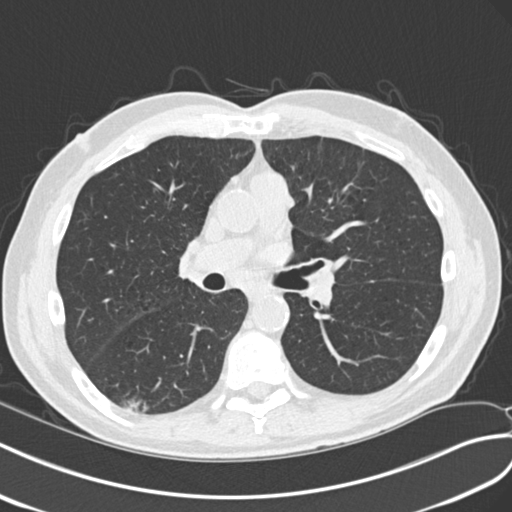
Low-dose screening chest CT, axial slice. Second screening round (one year after baseline). Lung window (W 1500 / L -600 HU). 2 mm slice thickness. Male, age 68 years at enrolment.
- Expert-annotated lung lesion, bounding box <112,385,162,422> (left, top, right, bottom; pixels).
- The screening reader recorded 4 non-calcified nodules or masses ≥4 mm on this exam; which of them this box marks is not recorded.
- Later outcome: lung cancer diagnosed 653 days after this screen (after the third annual screen) — non-small cell carcinoma, right lower lobe, poorly differentiated (G3), stage IA (AJCC 6th edition), 23 mm at pathology.